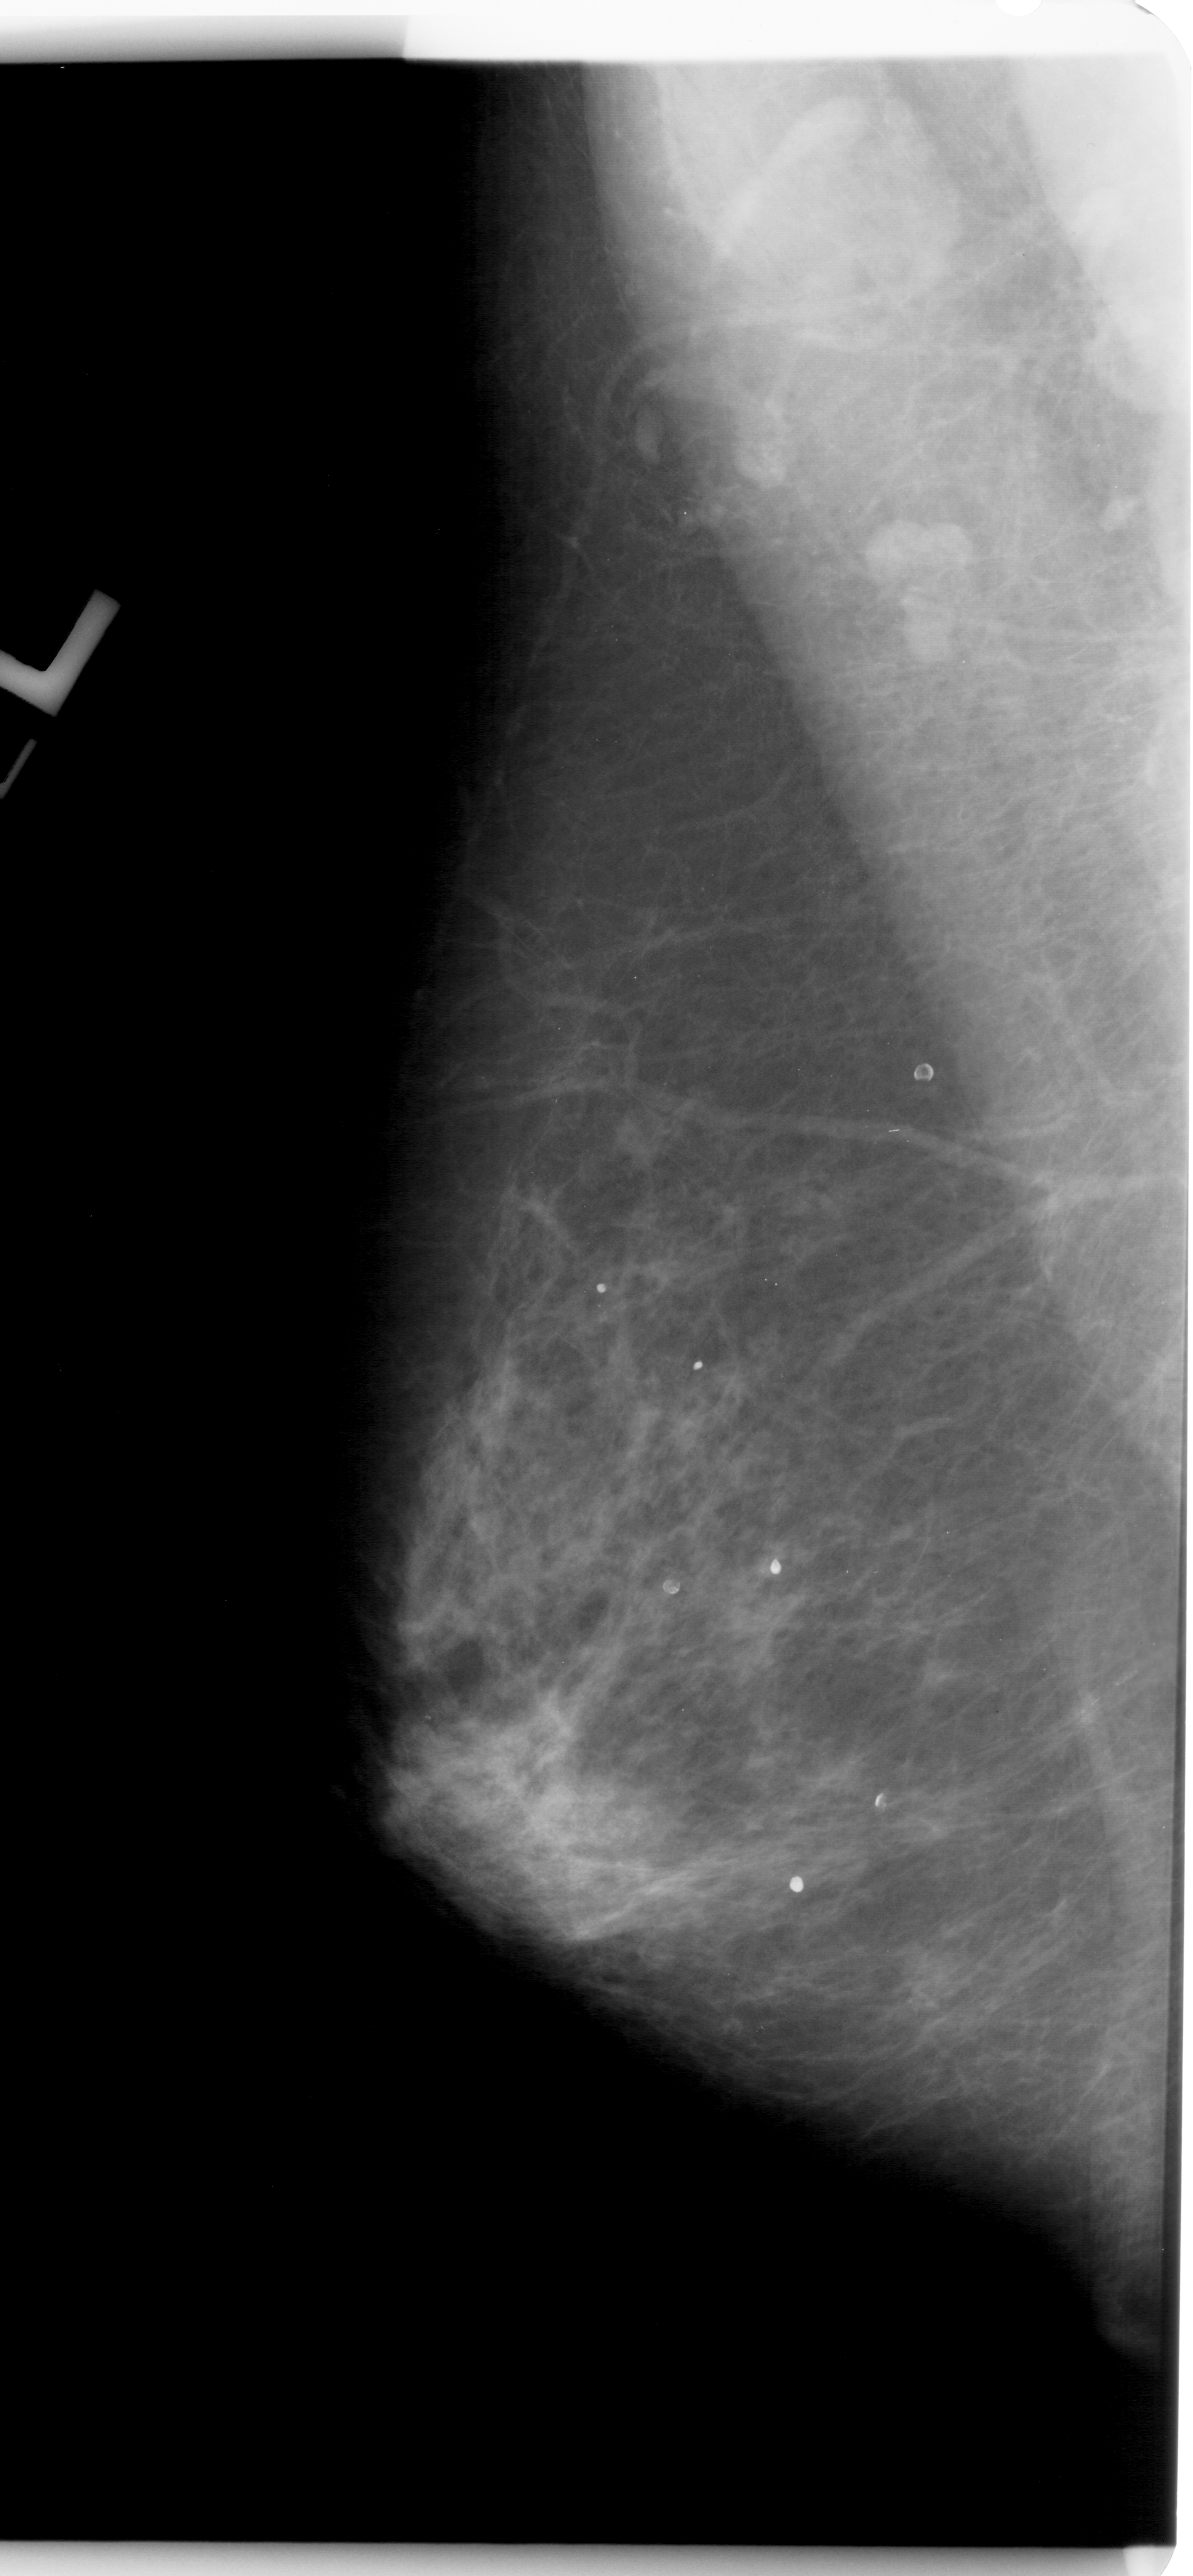
Mammogram (digitized film). Left breast. MLO view. Breast composition: heterogeneously dense (BI-RADS density category 3 of 4). 1193 × 2576 image matrix.
Expert-marked regions of interest on this film, with their recorded descriptors:
- mass, shape oval, margins ill defined; BI-RADS assessment category 4; pathology result (as recorded, not read from the image): malignant: box from (x=607, y=1106) to (x=675, y=1174) px